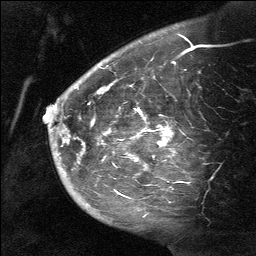
Breast MRI (dynamic contrast-enhanced), one sagittal slice. Position 47 of 64 along the scan axis. Dynamic contrast-enhanced study with each time point stored as its own series, time point 2 of 3 at this slice position (early post-contrast, ordered by acquisition time). 1.5 T. TE 4.8 ms, TR 27 ms. 2 mm slice thickness. 256 × 256 image matrix. Patient: female, 39 years. From the clinical record (not read from this slice): setting: breast cancer imaged before/during neoadjuvant chemotherapy; receptor status: HER2-positive.
Annotated regions visible in this slice (semi-automatic segmentation, software-assisted and operator-edited):
- analysis volume of interest (the breast-tissue region the enhancement analysis was run in; not a lesion): bounding box <58,40,200,217> (left, top, right, bottom; pixels)
- tumour enhancement mask (voxels above the 90 % enhancement threshold inside the analysis volume of interest): <98,87,167,157>